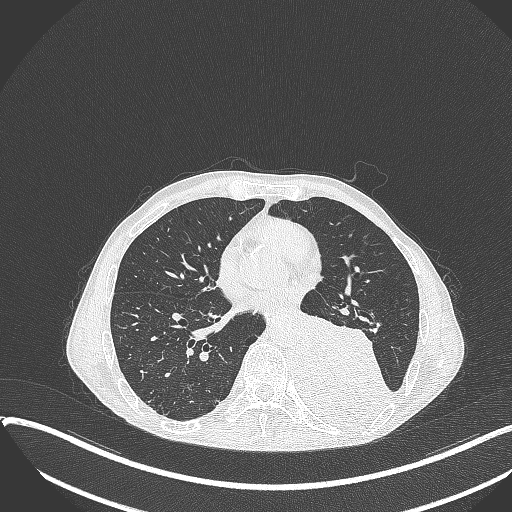
Chest CT, one axial slice. Slice 158 of 401 in the series (ordered by position). Reconstruction kernel B70f. Lung window (W 1500 / L -600 HU). 512 × 512 image matrix, field of view 400 × 400 mm. Male patient, age 57 years. From the clinical record (not read from this slice): clinical TNM (as recorded): T4 N0 M0.
Structures marked on this image (bounding box drawn by a radiologist):
- lung tumour (recorded histology: squamous cell carcinoma): box from (x=296, y=307) to (x=391, y=429) px